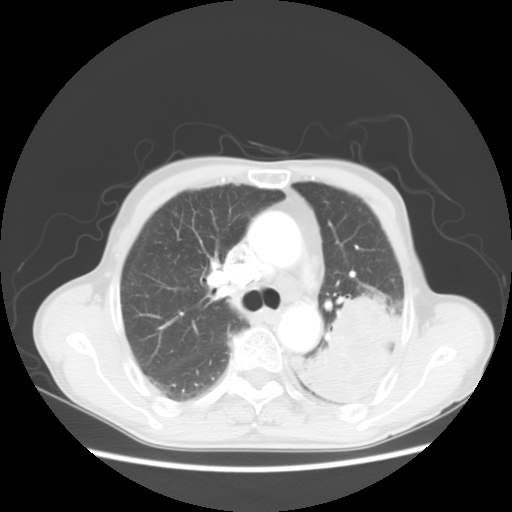
Chest CT, one axial slice. Slice 35 of 51 in the series (ordered by position). Reconstruction kernel STANDARD. 120 kVp. Lung window (W 1500 / L -600 HU). 5 mm slice thickness. 512 × 512 image matrix. Patient: male, 64 years. From the clinical record (not read from this slice): clinical TNM (as recorded): T4 N0 M0; histopathological grade: G2-3.
Annotated regions visible in this slice (bounding box drawn by a radiologist):
- lung tumour (recorded histology: squamous cell carcinoma): box from (x=310, y=292) to (x=394, y=395) px